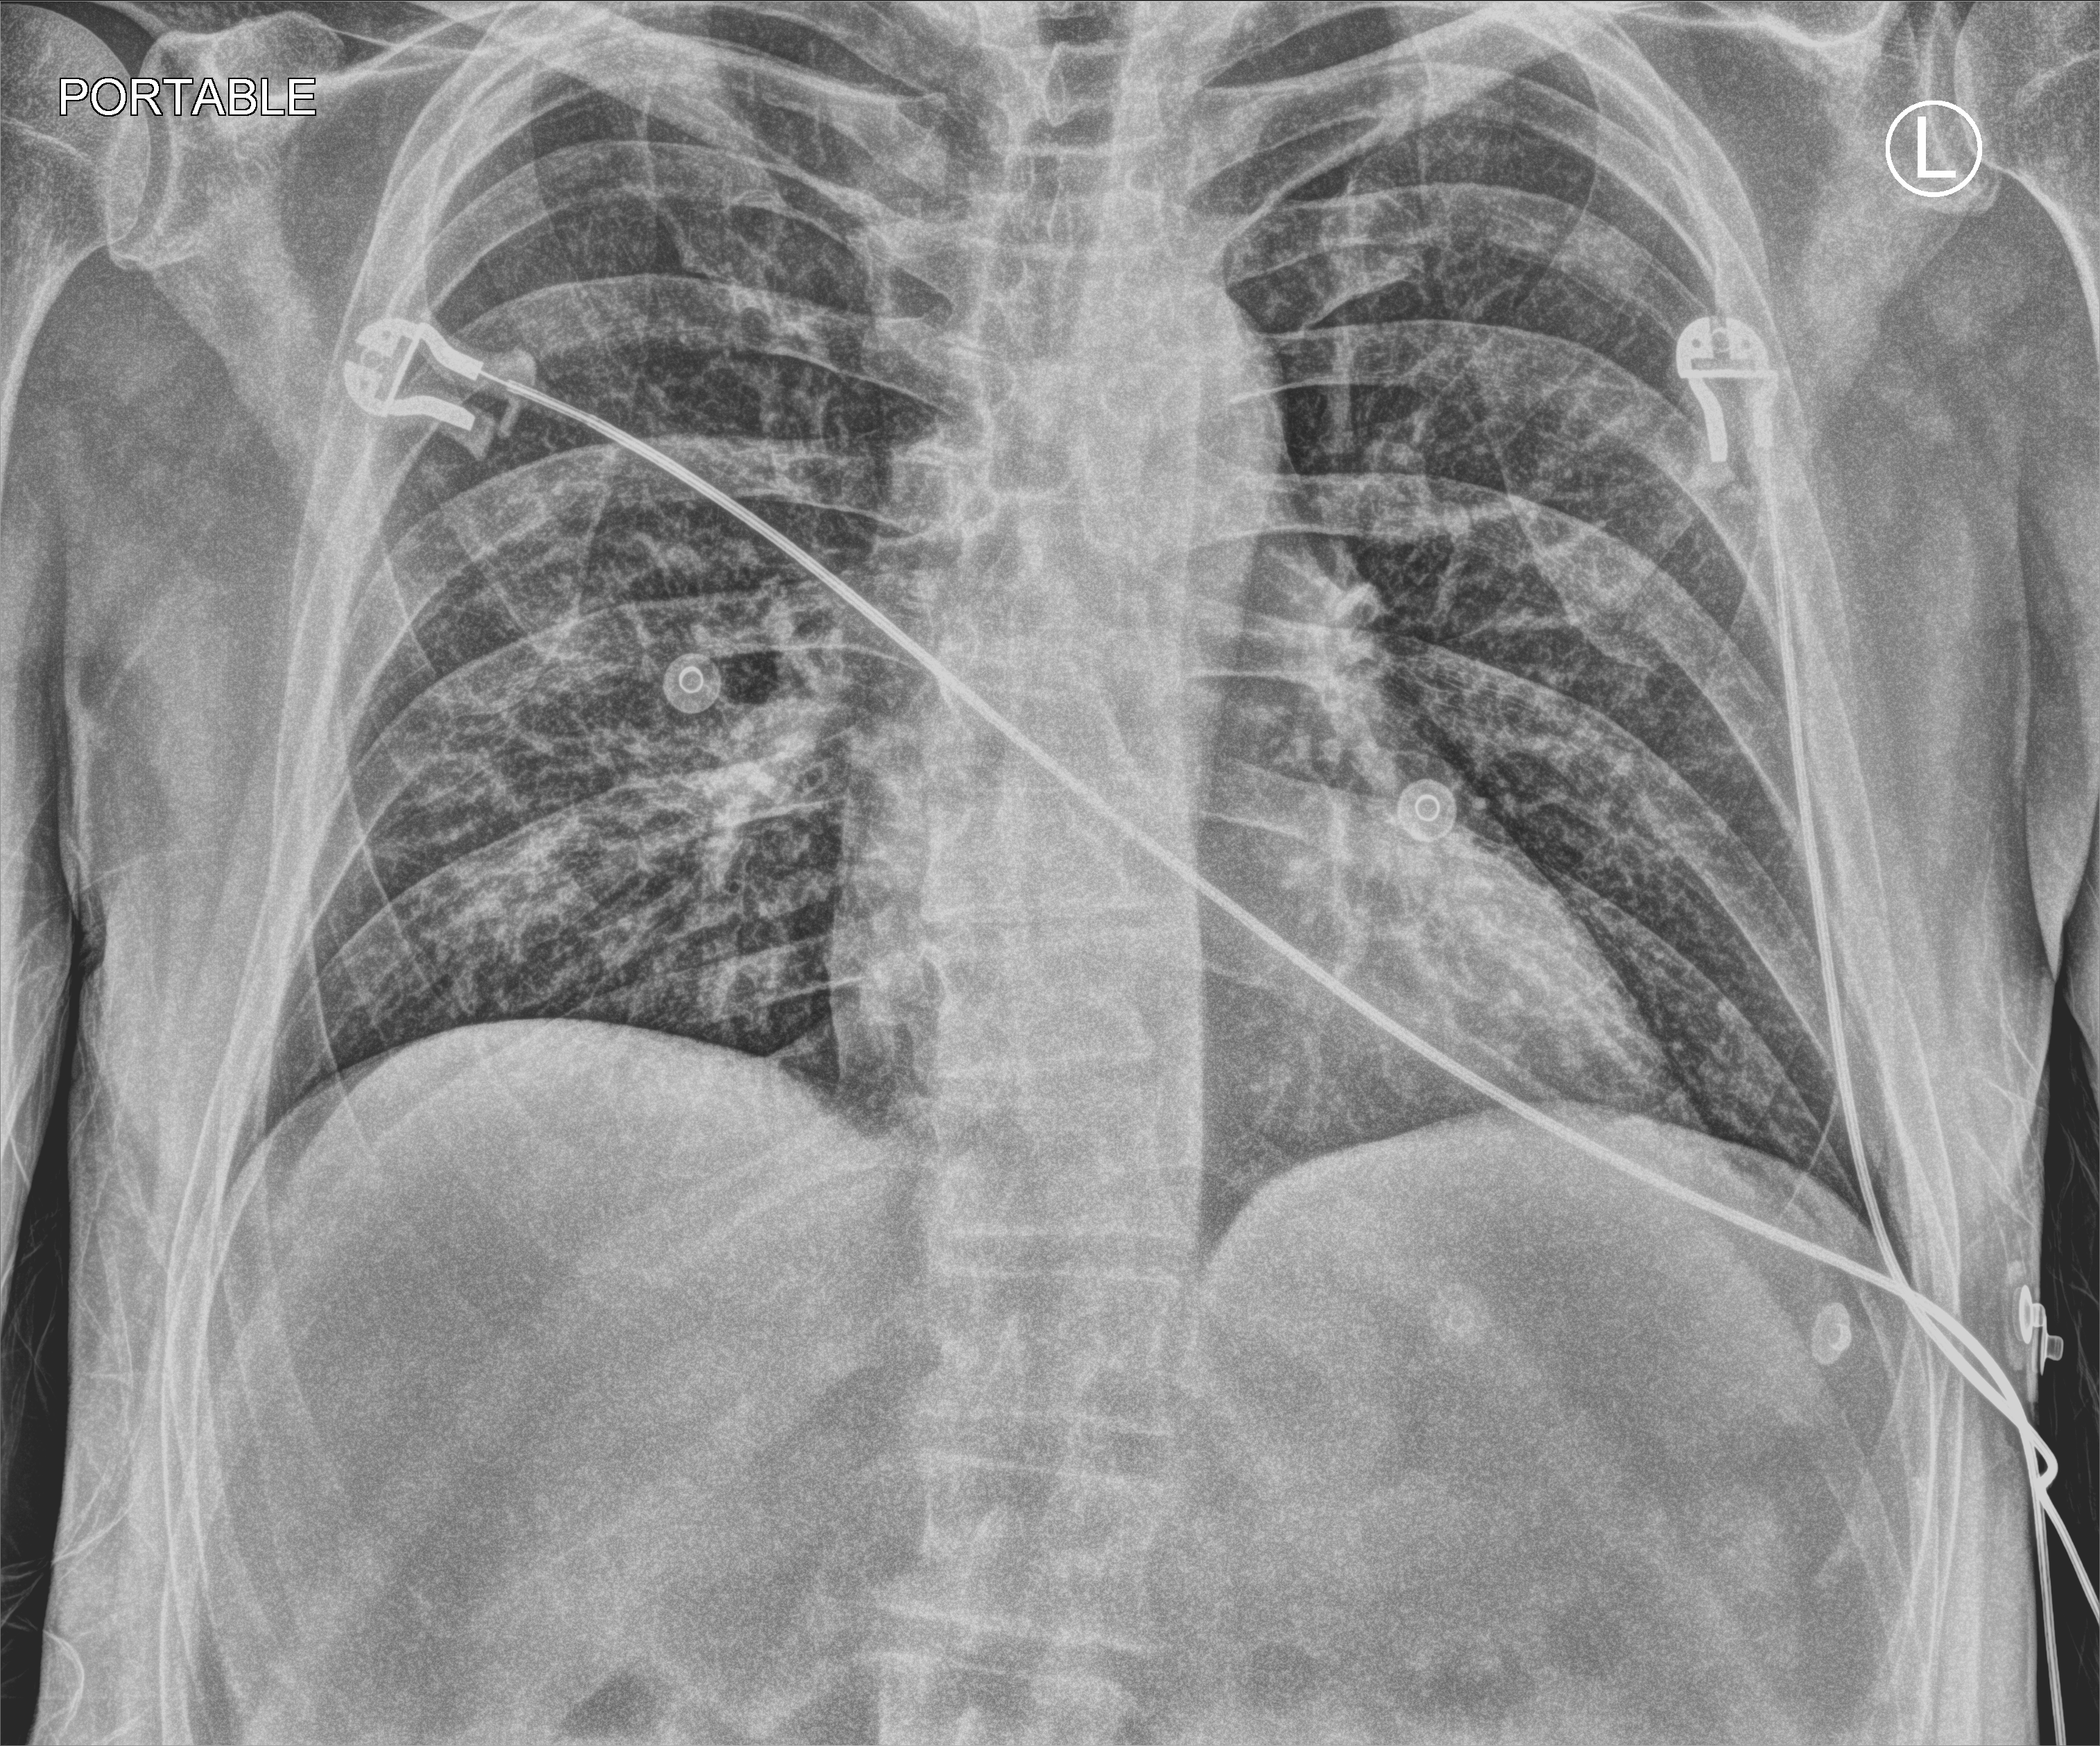
Bedside chest radiograph (computed radiography), anteroposterior (AP) projection. Patient hospitalised with COVID-19; male, aged 60–74 years.
Admission-level facts for this patient (not findings on this image; timing relative to this image not recorded): mechanically ventilated during this hospital stay: no.